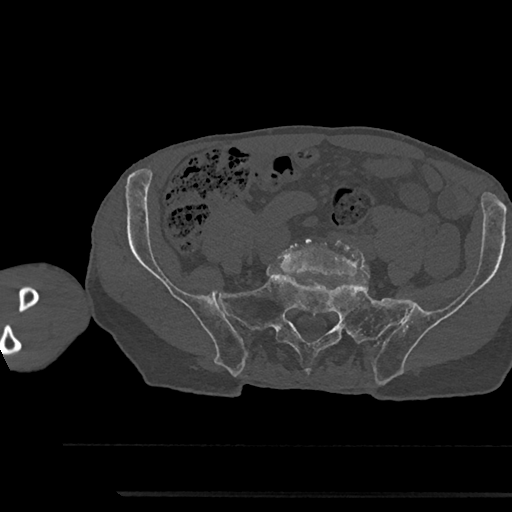
CT including the spine, one axial slice; slice 302 of 797 in the series (ordered by position); reconstruction kernel Br40s/3; 120 kVp; bone window (W 1800 / L 400 HU); 0.5 mm slice thickness; 512 × 512 image matrix, field of view 367 × 367 mm. Male patient, age 79 years. From the clinical record (not read from this slice): primary cancer: prostate.
Structures marked on this image (semi-automatic segmentation, software-assisted and operator-edited):
- L5 vertebra: bounding box (x1, y1, x2, y2) in pixels: (279, 236, 369, 276)